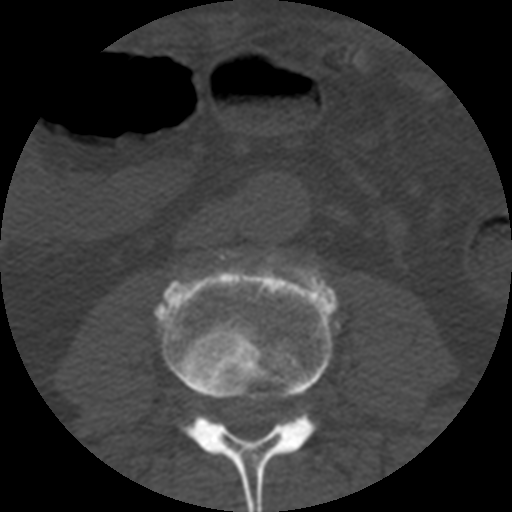
CT including the spine, one axial slice; slice 116 of 508 in the series (ordered by position); bone window (W 1800 / L 400 HU); 1.25 mm slice thickness; 512 × 512 image matrix, field of view 160 × 160 mm. Patient age 57 years. From the clinical record (not read from this slice): primary cancer: prostate.
Annotated regions visible in this slice (semi-automatic segmentation, software-assisted and operator-edited):
- L3 vertebra: box from (x=155, y=255) to (x=337, y=512) px